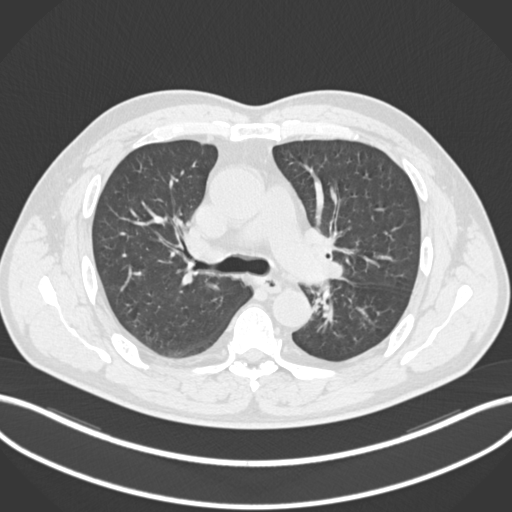
Chest CT, one axial slice. Slice 146 of 223 in the series (ordered by position). Reconstruction kernel B30f. Lung window (W 1500 / L -600 HU). 1 mm slice thickness. 512 × 512 image matrix, field of view 400 × 400 mm. Patient: male, 50 years. Case-level facts recorded for this patient, not image findings: clinical TNM (as recorded): T2a N3 M0.
Structures marked on this image (rectangle marked by the reading radiologist):
- lung tumour (recorded histology: squamous cell carcinoma): bounding box [x1, y1, x2, y2] px = [308, 283, 334, 328]